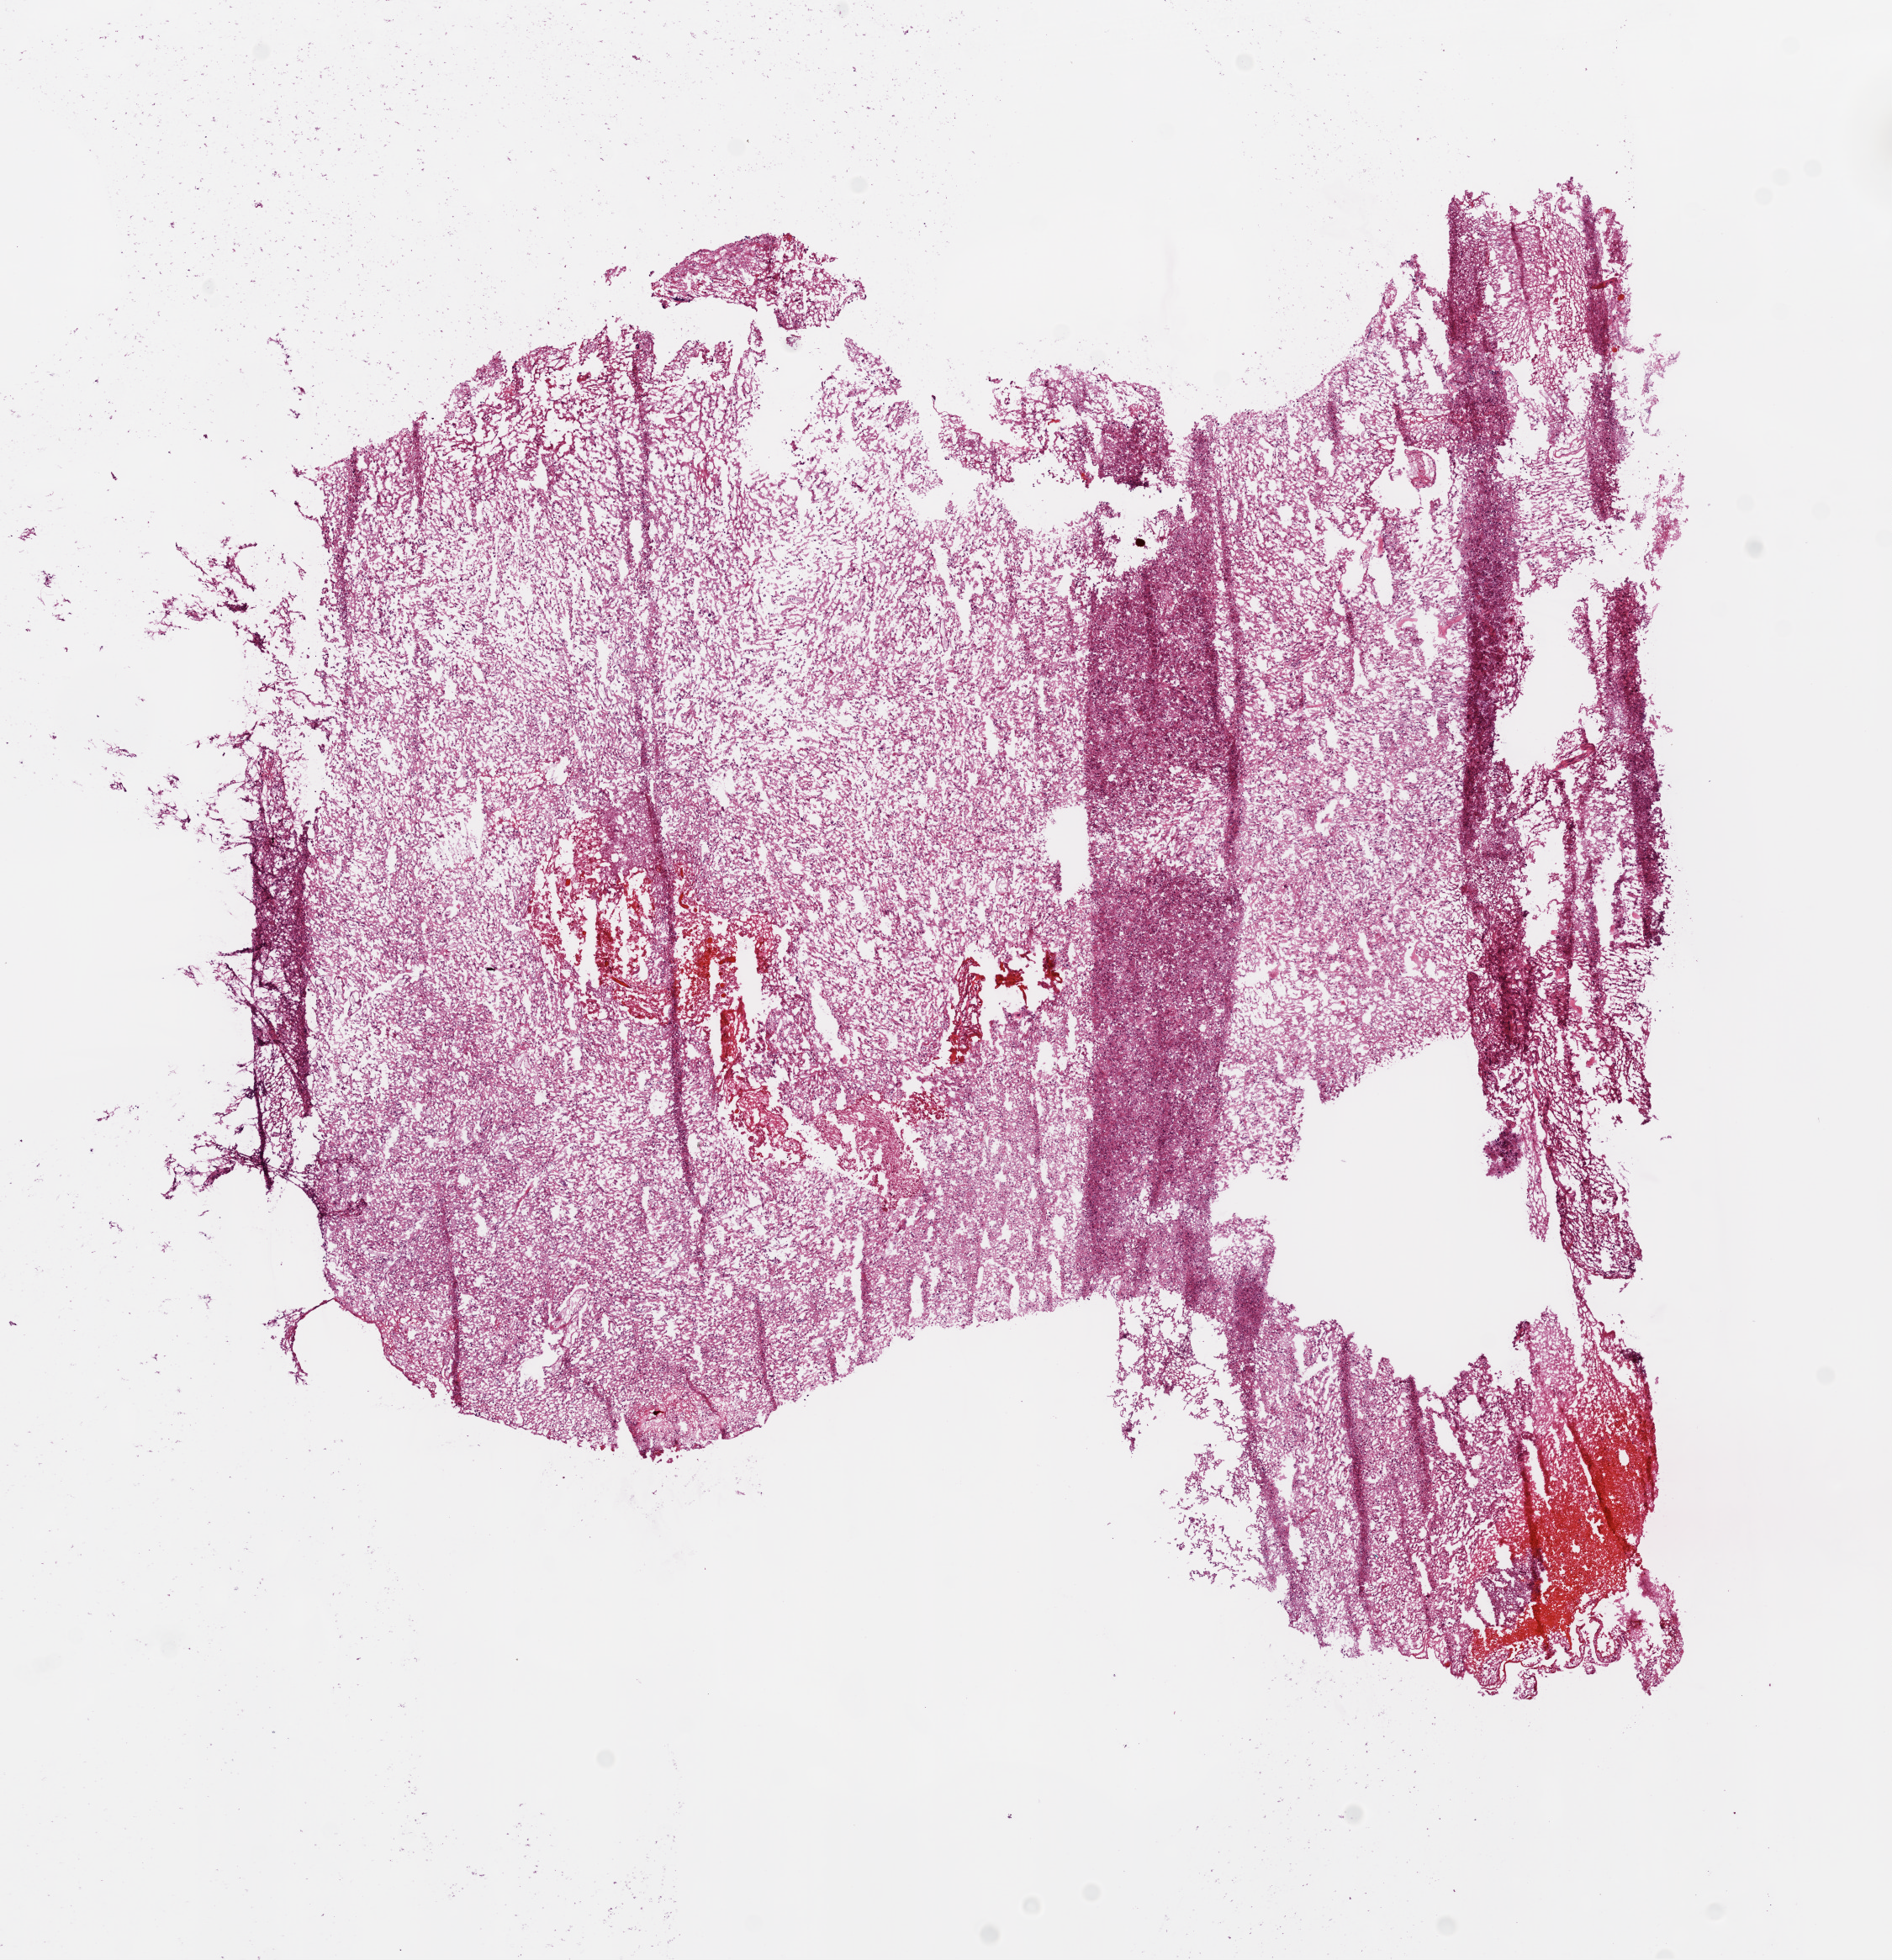
Whole-slide histology image, Hematoxylin and eosin (H&E) stained, whole scanned area (about 9.0 x 9.4 mm, acquisition: 20x scan) shown as a low-resolution overview; frozen section from the bottom of the tissue portion; brain, primary tumour sample. Male, age 64 years at initial diagnosis. Slide review estimates, as recorded: tumour cells 100%, tumour nuclei 80%, normal cells 0%, stromal cells 0%, necrosis 0%.
Diagnosis: Glioblastoma.